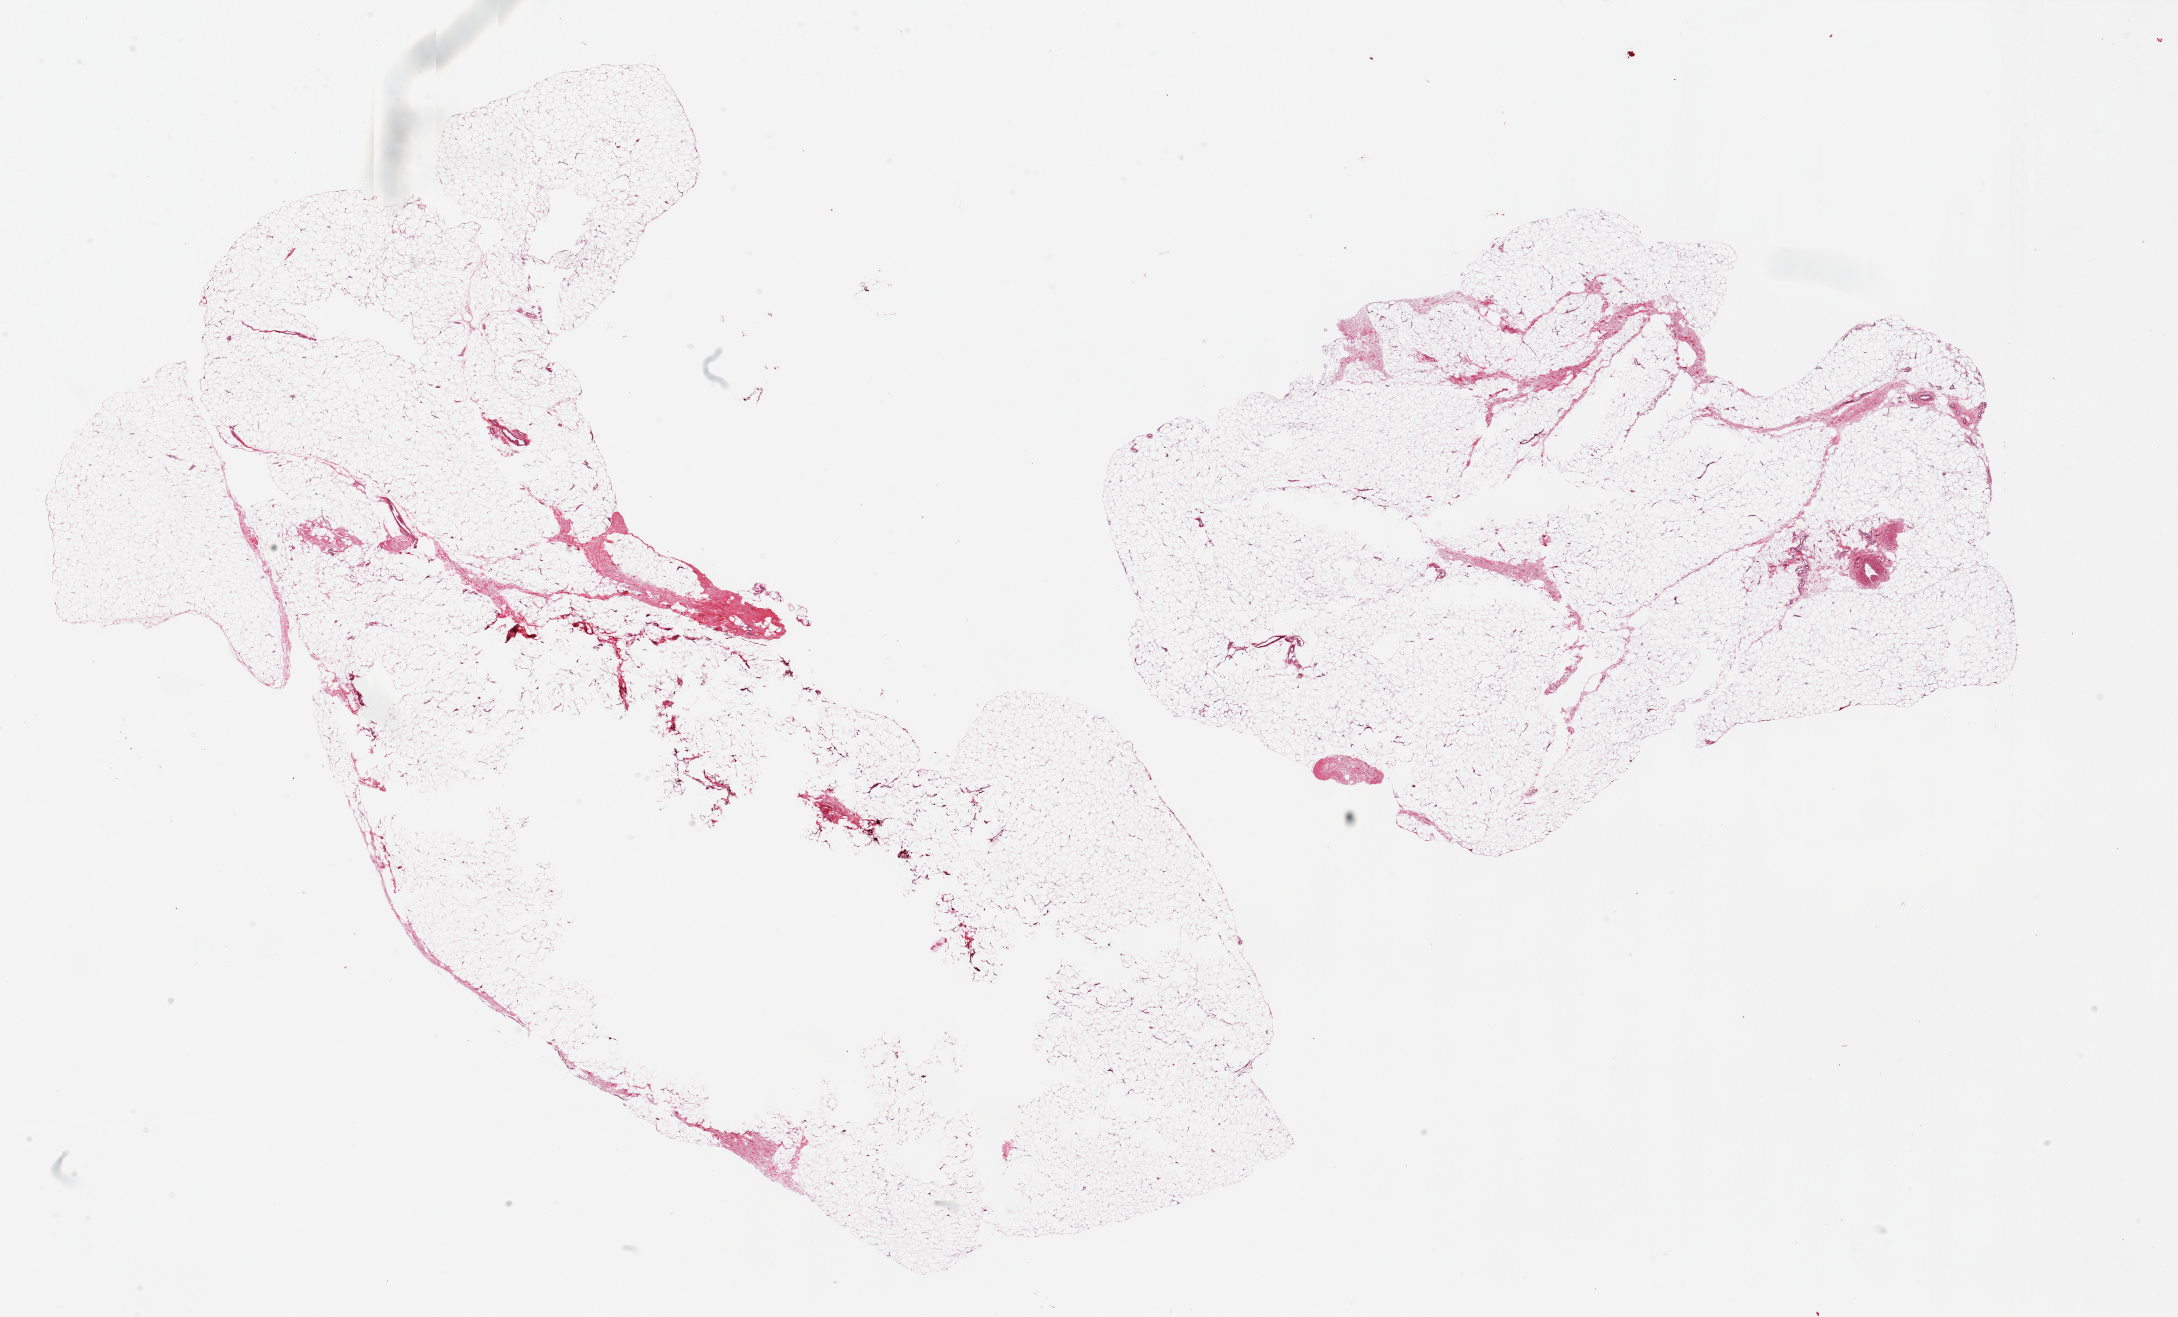
Whole-slide image, H&E stain, a low-resolution overview of the entire scanned area, about 34.5 x 20.8 mm (slide scanned at 20x); PAXgene-fixed, paraffin-embedded tissue; target tissue: adipose tissue; tissue donor sample. Male donor.
Review note (as recorded): 2 pieces, <10% fascia/vascular elements.